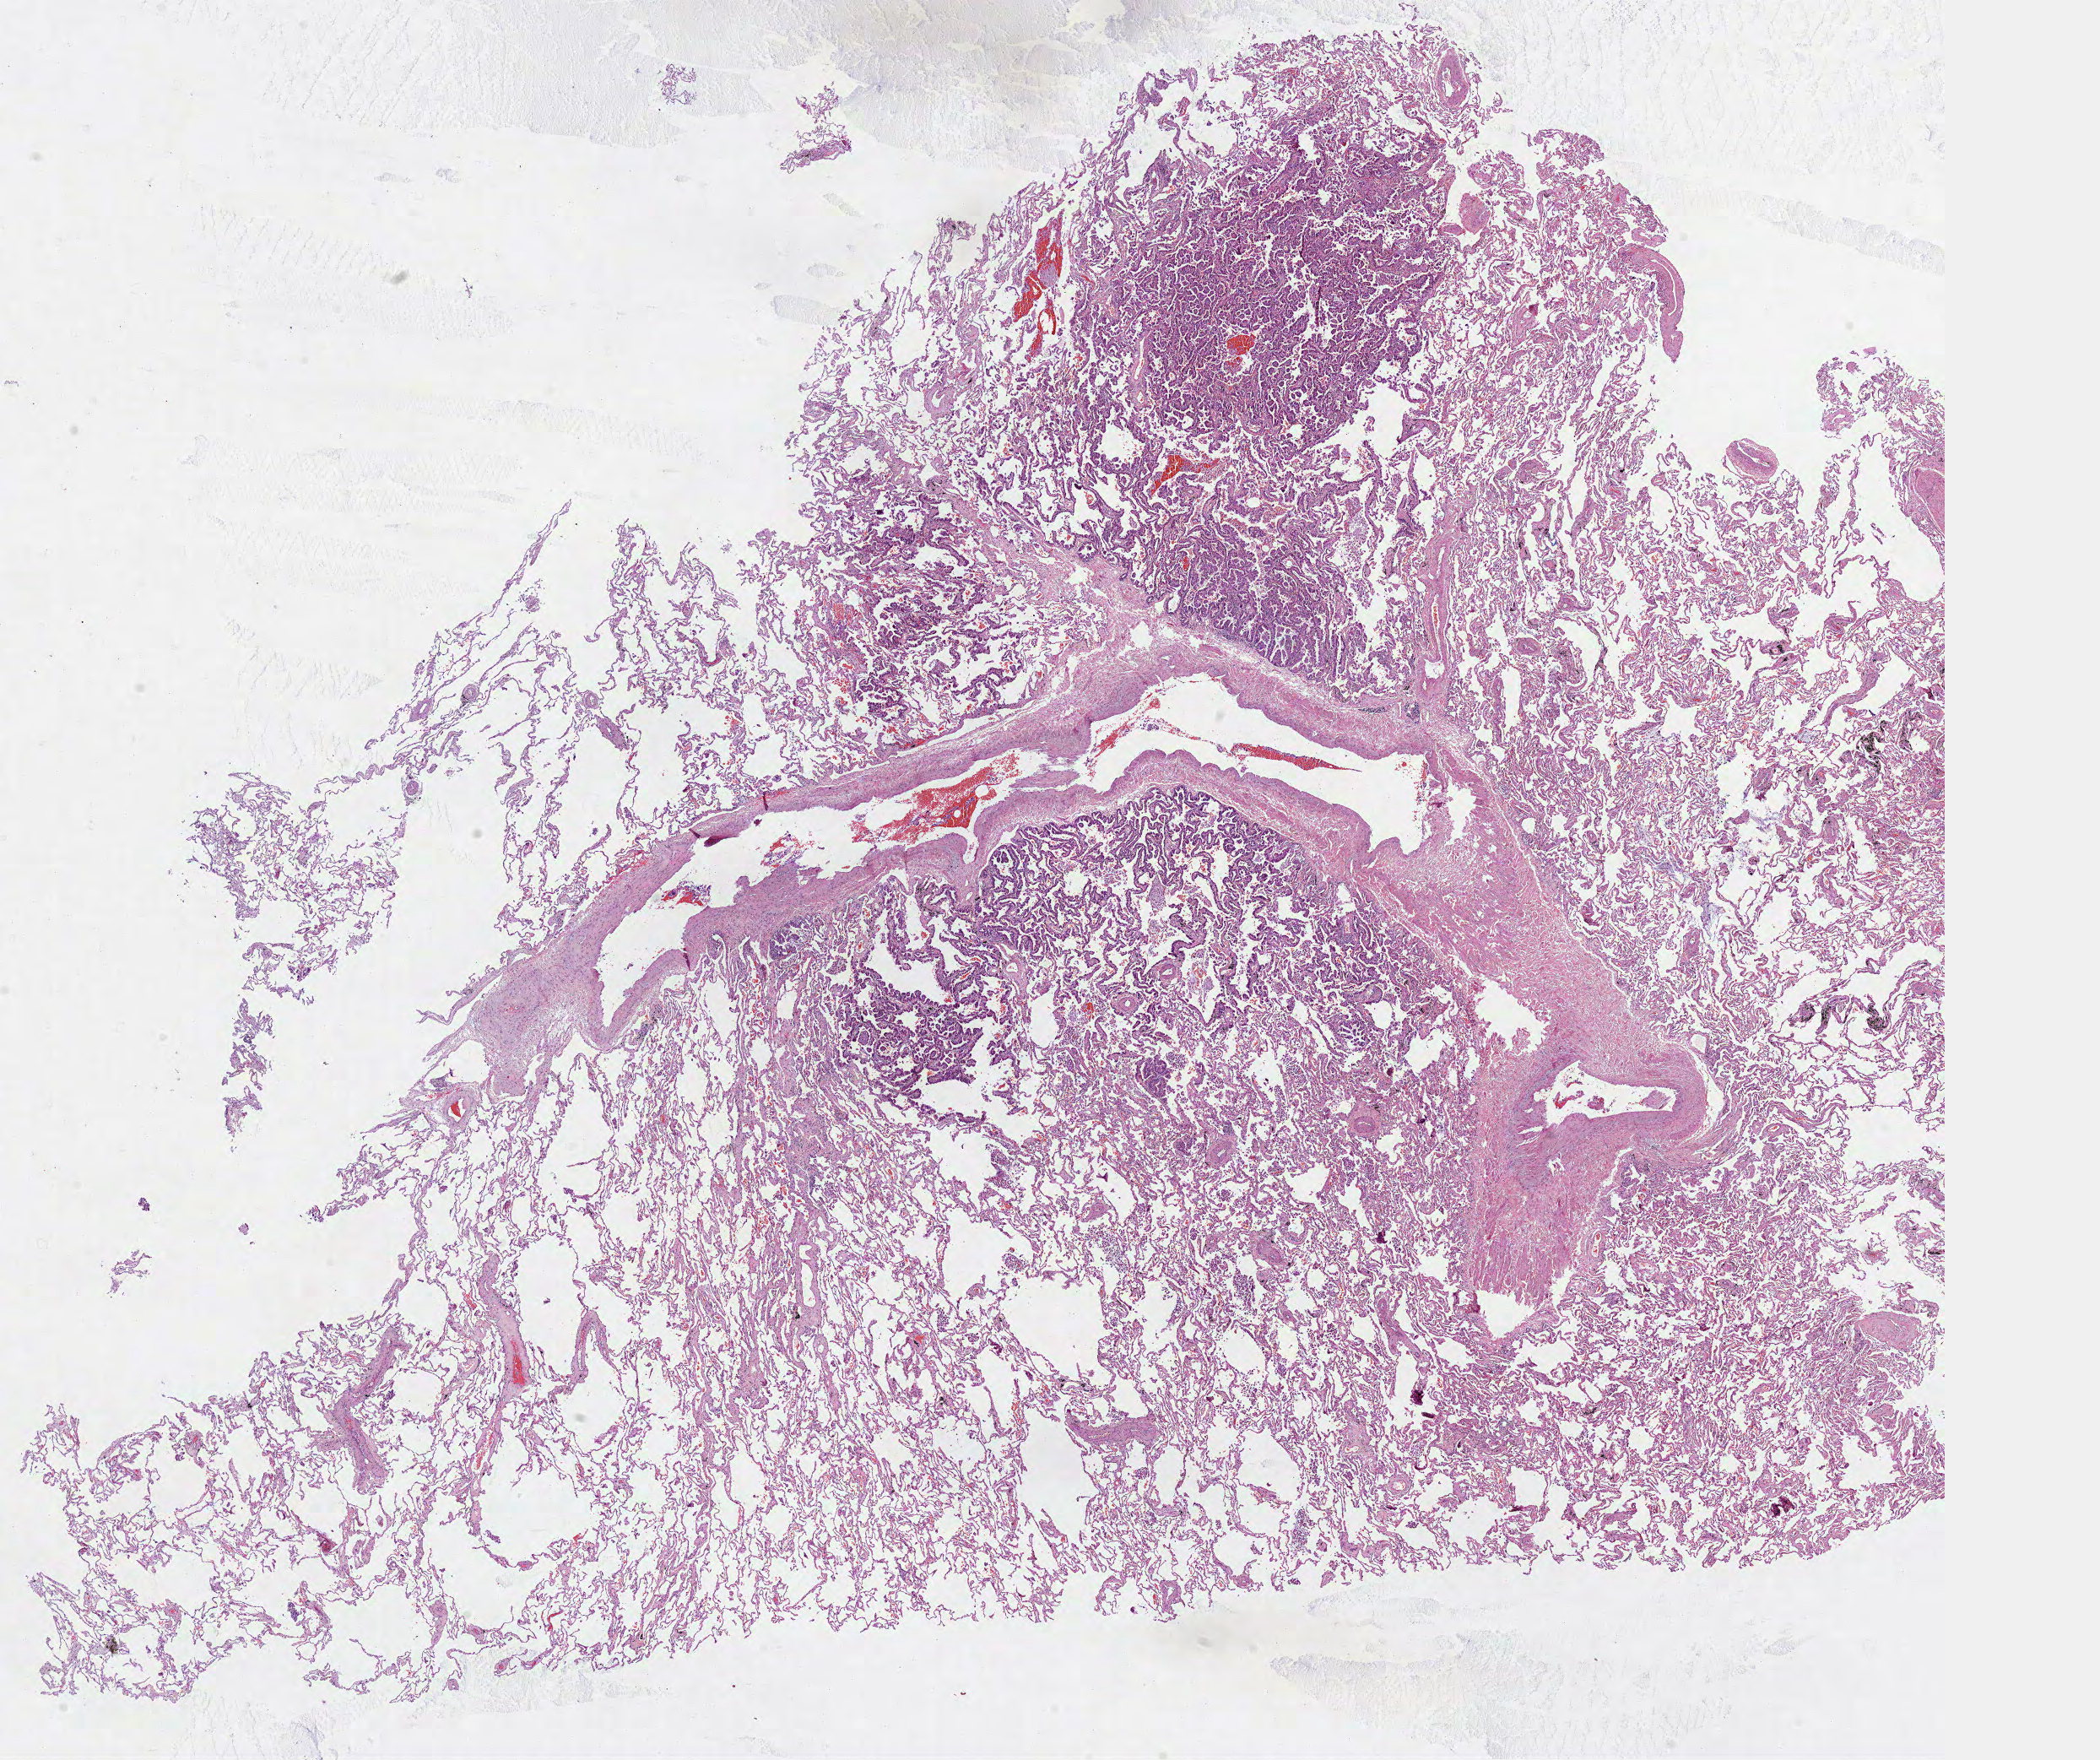
Hematoxylin and eosin (H&E) stained whole-slide image — a low-resolution overview of the entire scanned area, about 20.1 x 16.8 mm (from a 40x scan), formalin-fixed paraffin-embedded (FFPE) diagnostic section, sample: primary tumour, lung. Patient: female, age at initial diagnosis 70 years.
Histologic diagnosis: Adenocarcinoma, NOS (upper lobe, lung). AJCC pathologic stage: IA (7th edition).